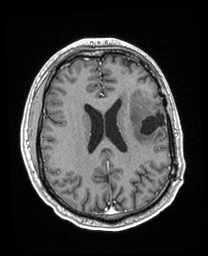
Brain MRI from a brain-tumour surgery series, one axial slice; slice 88 of 208 in the series (ordered by position); T1-weighted post-contrast; 1 mm slice thickness; 208 × 256 image matrix. From the clinical record (not read from this slice): histopathology: Astrocytoma; WHO grade: 3; IDH mutation: yes; tumour location: Left Insular.
Outlined on this slice (outlined manually by an expert reader):
- previous resection cavity: bounding box <140,113,165,136> (left, top, right, bottom; pixels)